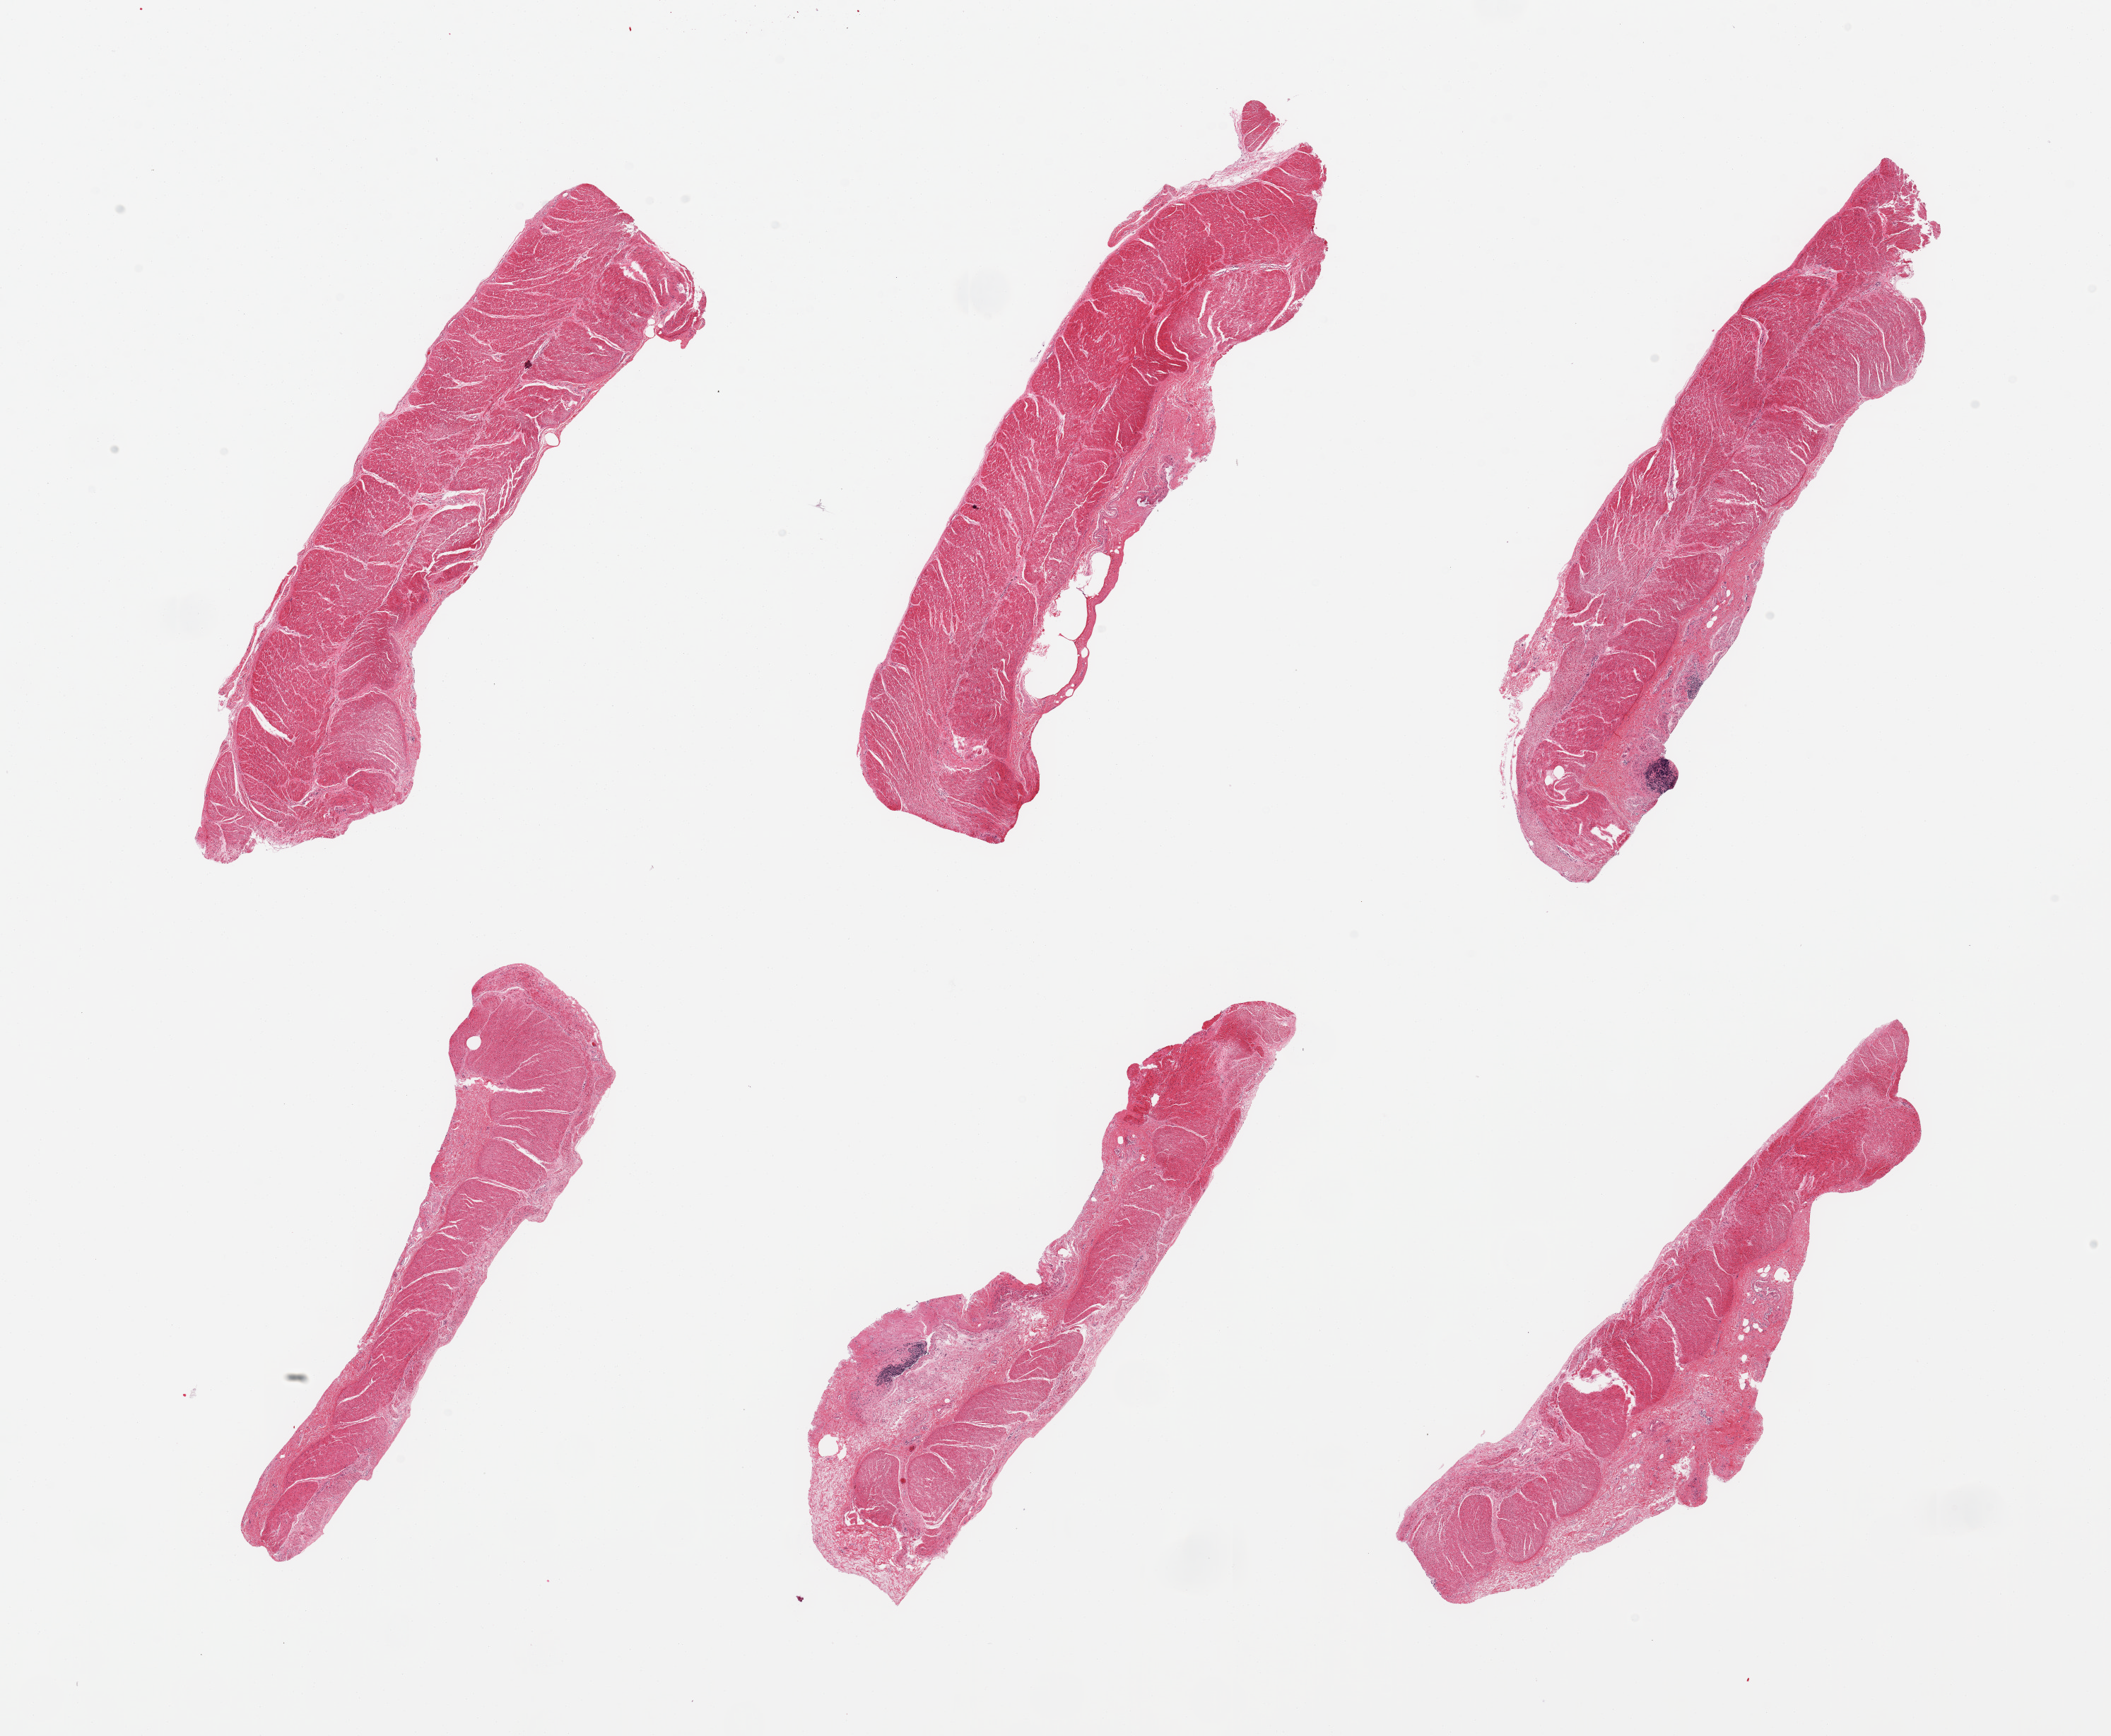
Hematoxylin and eosin (H&E) whole-slide image — a low-resolution overview of the entire scanned area, about 23.6 x 19.4 mm. PAXgene-fixed, paraffin-embedded tissue. Target tissue: sigmoid colon. Donor tissue sample. Donor: female.
Reviewer comment on this tissue sample: 6 pieces; well dissected muscle.